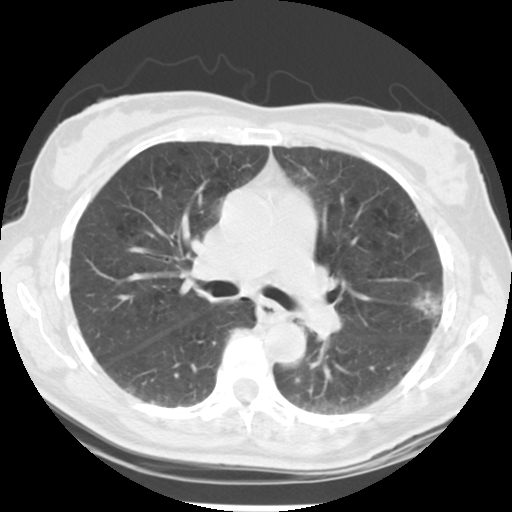
Axial slice from a low-dose chest CT screening exam. Second annual screen. Lung window (W 1500 / L -600 HU). 2.5 mm slice thickness. Standard (soft-tissue) reconstruction kernel (STANDARD). 120 kVp. Slice 132 of 223 in the series. 512 × 512 image matrix. Female participant, aged 61 years at enrolment. Current smoker at enrolment.
Expert reader's lesion annotation, box from (x=404, y=278) to (x=464, y=339) px. Reader record for this screening exam (exam-level; its link to the box is not recorded): non-calcified nodule or mass ≥4 mm, left upper lobe, 15 × 15 mm, poorly defined margins, mixed attenuation, pre-existing on the prior screen: no. Later outcome: lung cancer diagnosed 152 days after this screen — bronchiolo-alveolar adenocarcinoma, NOS, left upper lobe, well differentiated (G1), stage IA (AJCC 6th edition), 11 mm at pathology.